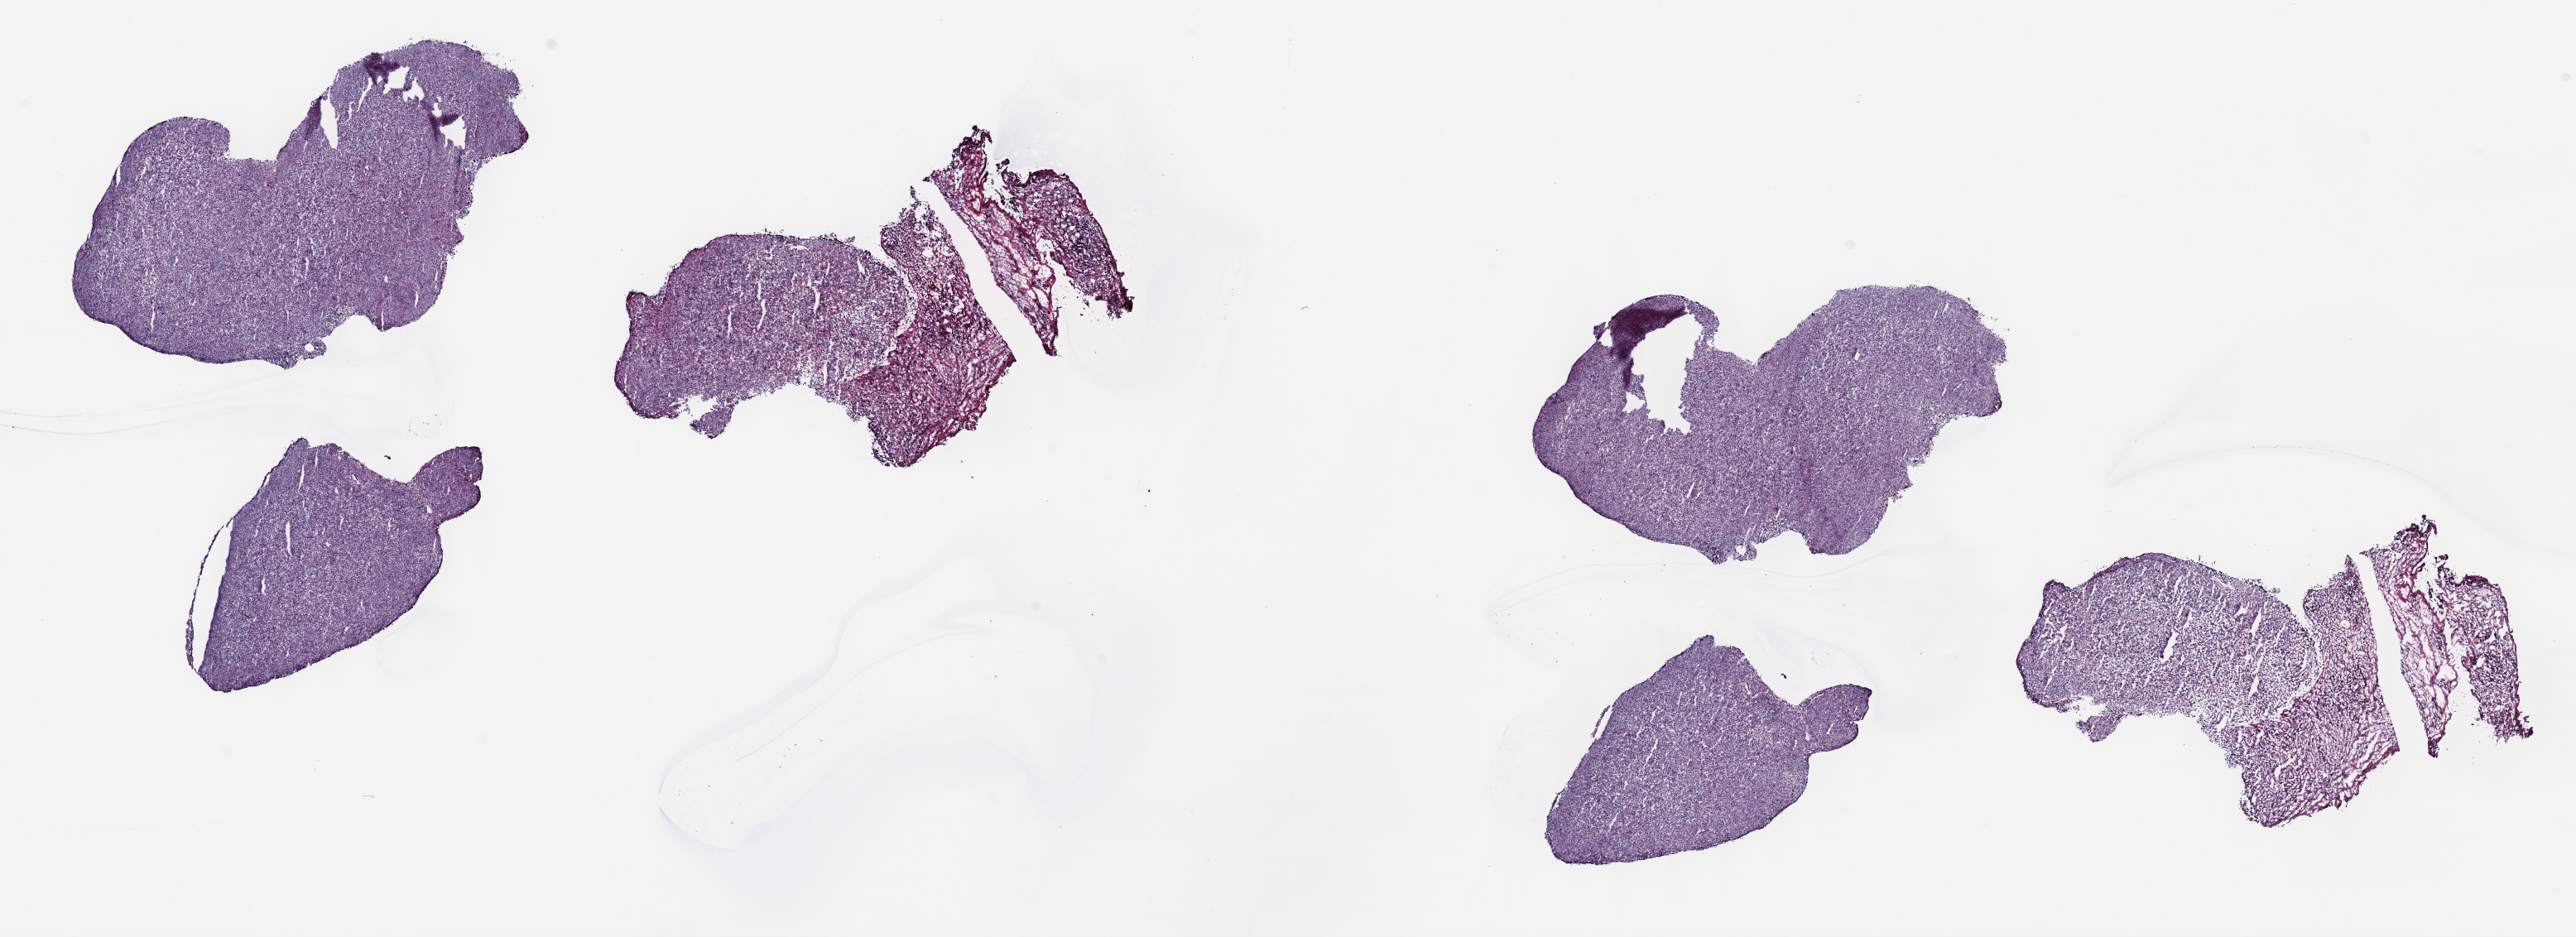
Digitized H&E-stained tissue section (whole slide) — low-resolution overview of the scanned area, about 25.2 x 9.2 mm (acquisition: 40x scan). Frozen section from the top of the tissue portion. Sample: primary tumour, lymphoid tissue. Patient: male, age at initial diagnosis 45 years. Pathologist review of this section (percent, as recorded): tumour cells 80%, tumour nuclei 90%.
Histologic diagnosis: Diffuse large B-cell lymphoma, NOS (lymph nodes of inguinal region or leg).